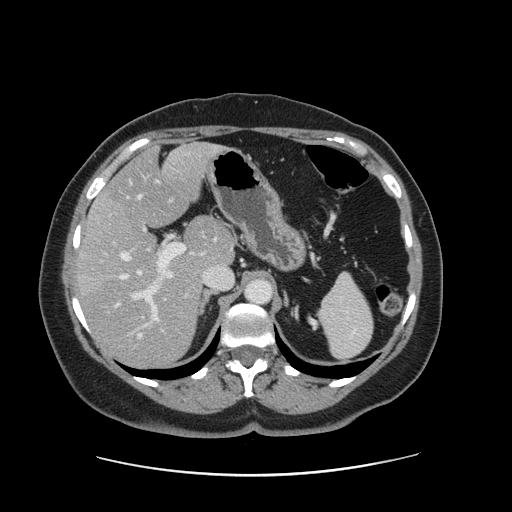
Contrast-enhanced abdominal CT, one axial slice; slice 94 of 161 in the series (ordered by position); intravenous contrast given; soft-tissue window (W 400 / L 40 HU); 2.5 mm slice thickness; 512 × 512 image matrix. Female patient, age 62 years. Case-level facts recorded for this patient, not image findings: diagnosis: colorectal cancer liver metastases, imaged before liver resection; multiple liver metastases: no; largest metastasis: 2.5 cm; chemotherapy before resection: yes.
Structures marked on this image (expert manual segmentation):
- hepatic veins: bounding box (x1, y1, x2, y2) in pixels: (118, 194, 142, 337)
- liver: (80, 144, 234, 366)
- planned liver remnant (the part of the liver to remain after resection): (105, 144, 233, 268)
- portal vein (with intrahepatic branches): (129, 236, 185, 336)